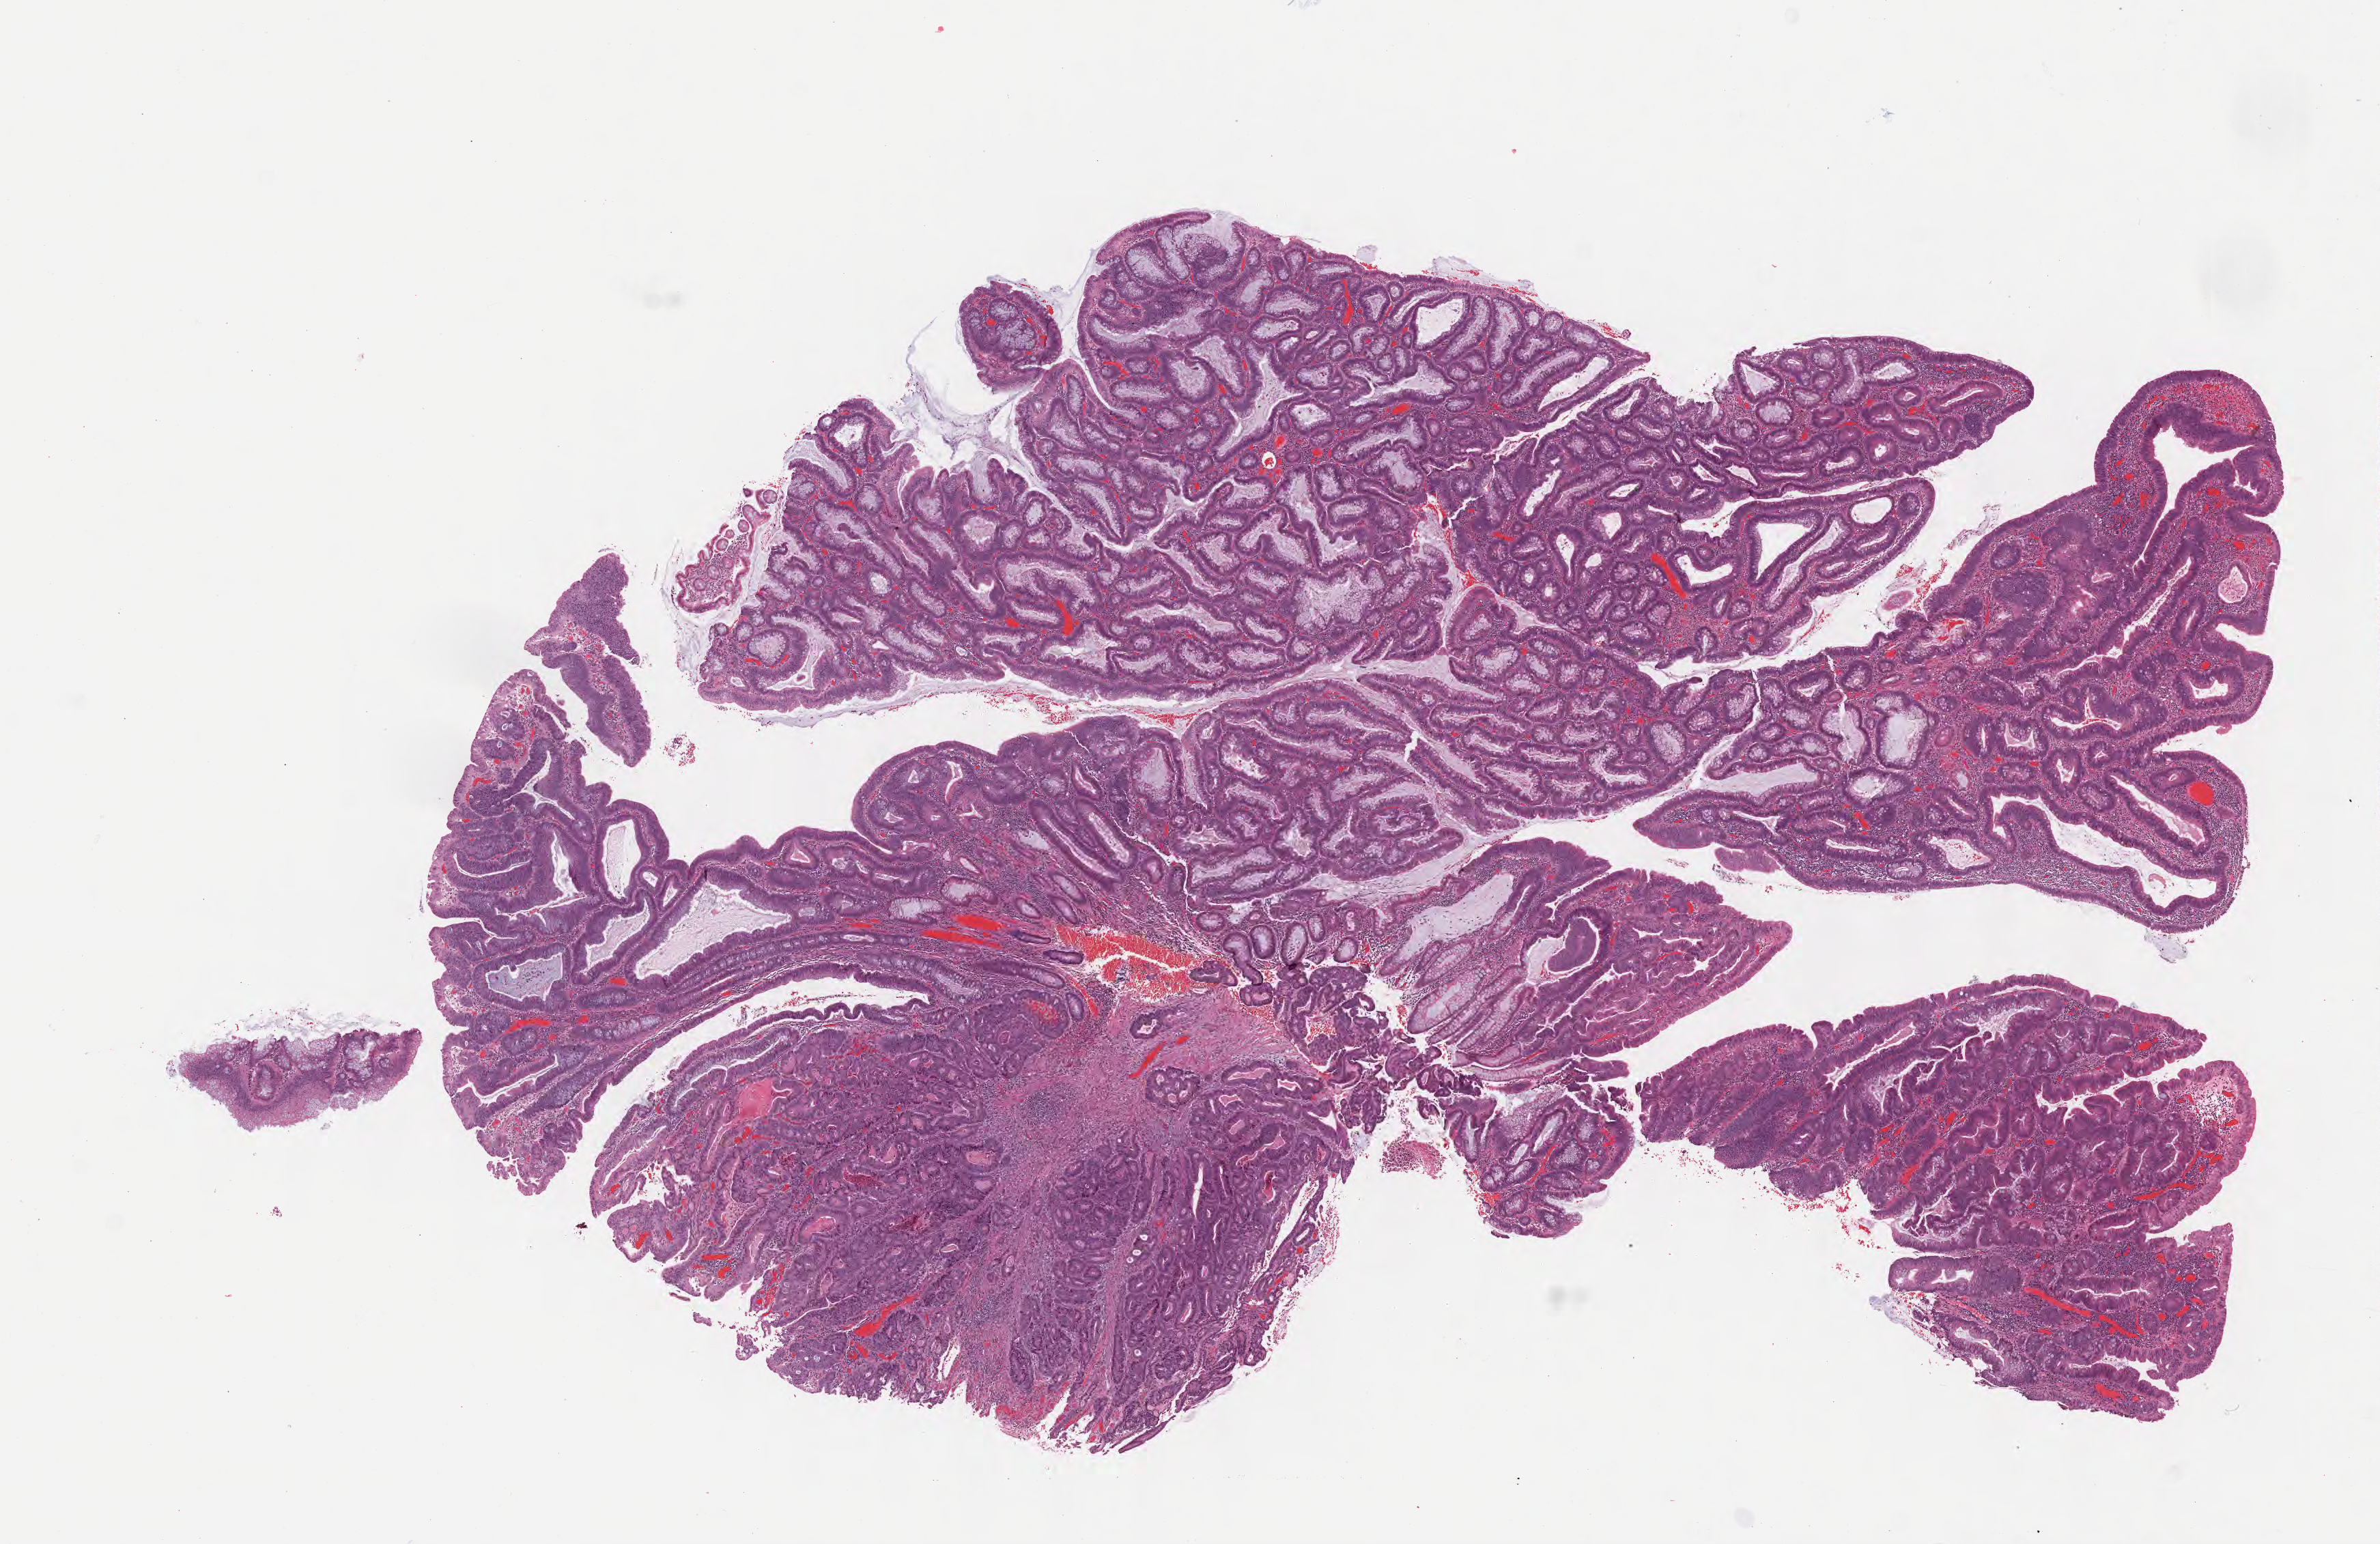
Haematoxylin and eosin whole-slide image, low-resolution overview of the scanned area, about 14.1 x 9.1 mm. Formalin-fixed paraffin-embedded section. Primary tumor. Site: cecum. Male, age 75 years at initial diagnosis. Pathologist review of this section (percent, as recorded): tumor cells 20%, tumor nuclei 20%.
Histologic diagnosis: Adenocarcinoma, NOS.